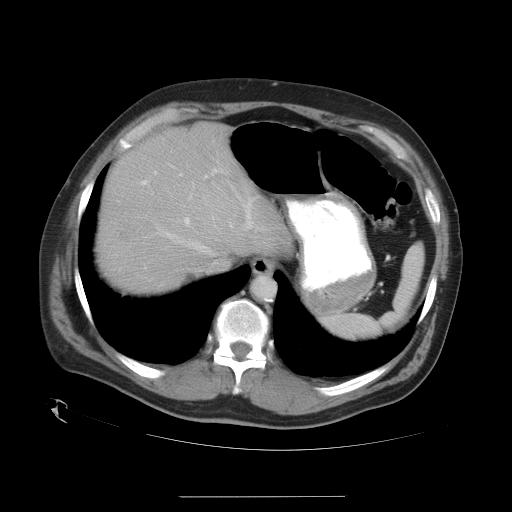
Contrast-enhanced abdominal CT, one axial slice; slice 27 of 35 in the series (ordered by position); reconstruction kernel STANDARD; 120 kVp; intravenous contrast given; soft-tissue window (W 400 / L 40 HU); 512 × 512 image matrix. Male patient, age 67 years. From the clinical record (not read from this slice): diagnosis: colorectal cancer liver metastases, imaged before liver resection; multiple liver metastases: no; largest metastasis: 2.3 cm; disease in both lobes: no.
Outlined on this slice (manually delineated by an expert):
- hepatic veins: bounding box (x1, y1, x2, y2) in pixels: (139, 171, 254, 254)
- liver: (98, 128, 286, 290)
- planned liver remnant (the part of the liver to remain after resection): (105, 129, 287, 290)
- portal vein (with intrahepatic branches): (180, 170, 254, 229)
- liver metastasis: (121, 227, 131, 243)